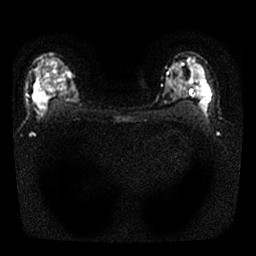
Breast MRI, one axial slice. Slice 18 of 25 in the series (ordered by position). Diffusion-weighted series; image 2 of 4 stored at this slice position (different b-values; order by instance number). 1.5 T. 4 mm slice thickness. 256 × 256 image matrix, field of view 300 × 300 mm. Female patient.
Outlined on this slice (outlined manually by an expert reader):
- tumour on diffusion-weighted imaging: bounding box <33,72,78,103> (left, top, right, bottom; pixels)